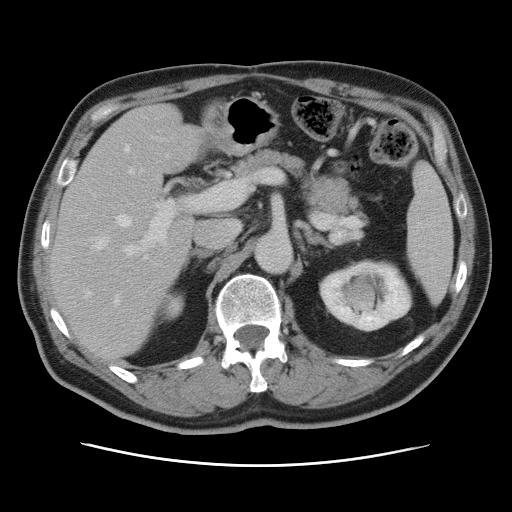
Contrast-enhanced abdominal CT, one axial slice; position 45 of 80 along the scan axis; 120 kVp; intravenous contrast given; soft-tissue window (W 400 / L 40 HU); 5 mm slice thickness; 512 × 512 image matrix, field of view 370 × 370 mm. Male patient, age 69 years. From the clinical record (not read from this slice): diagnosis: colorectal cancer liver metastases, imaged before liver resection; multiple liver metastases: no; largest metastasis: 5 cm; disease in both lobes: yes.
Outlined on this slice (manually delineated by an expert):
- hepatic veins: bounding box (x1, y1, x2, y2) in pixels: (95, 146, 147, 304)
- liver: (50, 105, 202, 357)
- planned liver remnant (the part of the liver to remain after resection): (51, 127, 203, 356)
- portal vein (with intrahepatic branches): (123, 168, 205, 257)